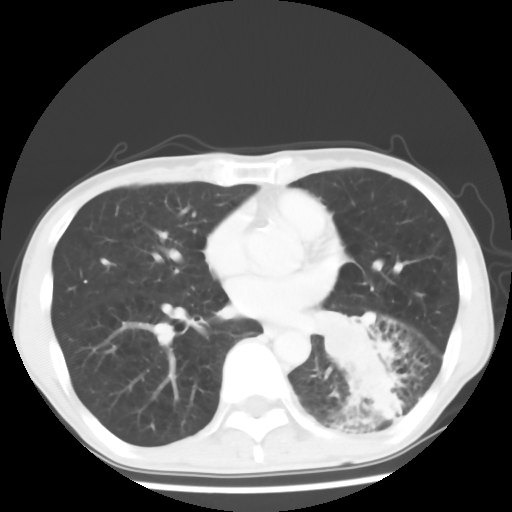
Chest CT, one axial slice. Slice 28 of 64 in the series (ordered by position). 120 kVp. Lung window (W 1500 / L -600 HU). 512 × 512 image matrix, field of view 313 × 313 mm. Male patient, age 68 years. Case-level facts recorded for this patient, not image findings: clinical TNM (as recorded): T4 N0 M0.
Structures marked on this image (bounding box drawn by a radiologist):
- lung tumour (recorded histology: squamous cell carcinoma): bounding box <315,300,384,378> (left, top, right, bottom; pixels)